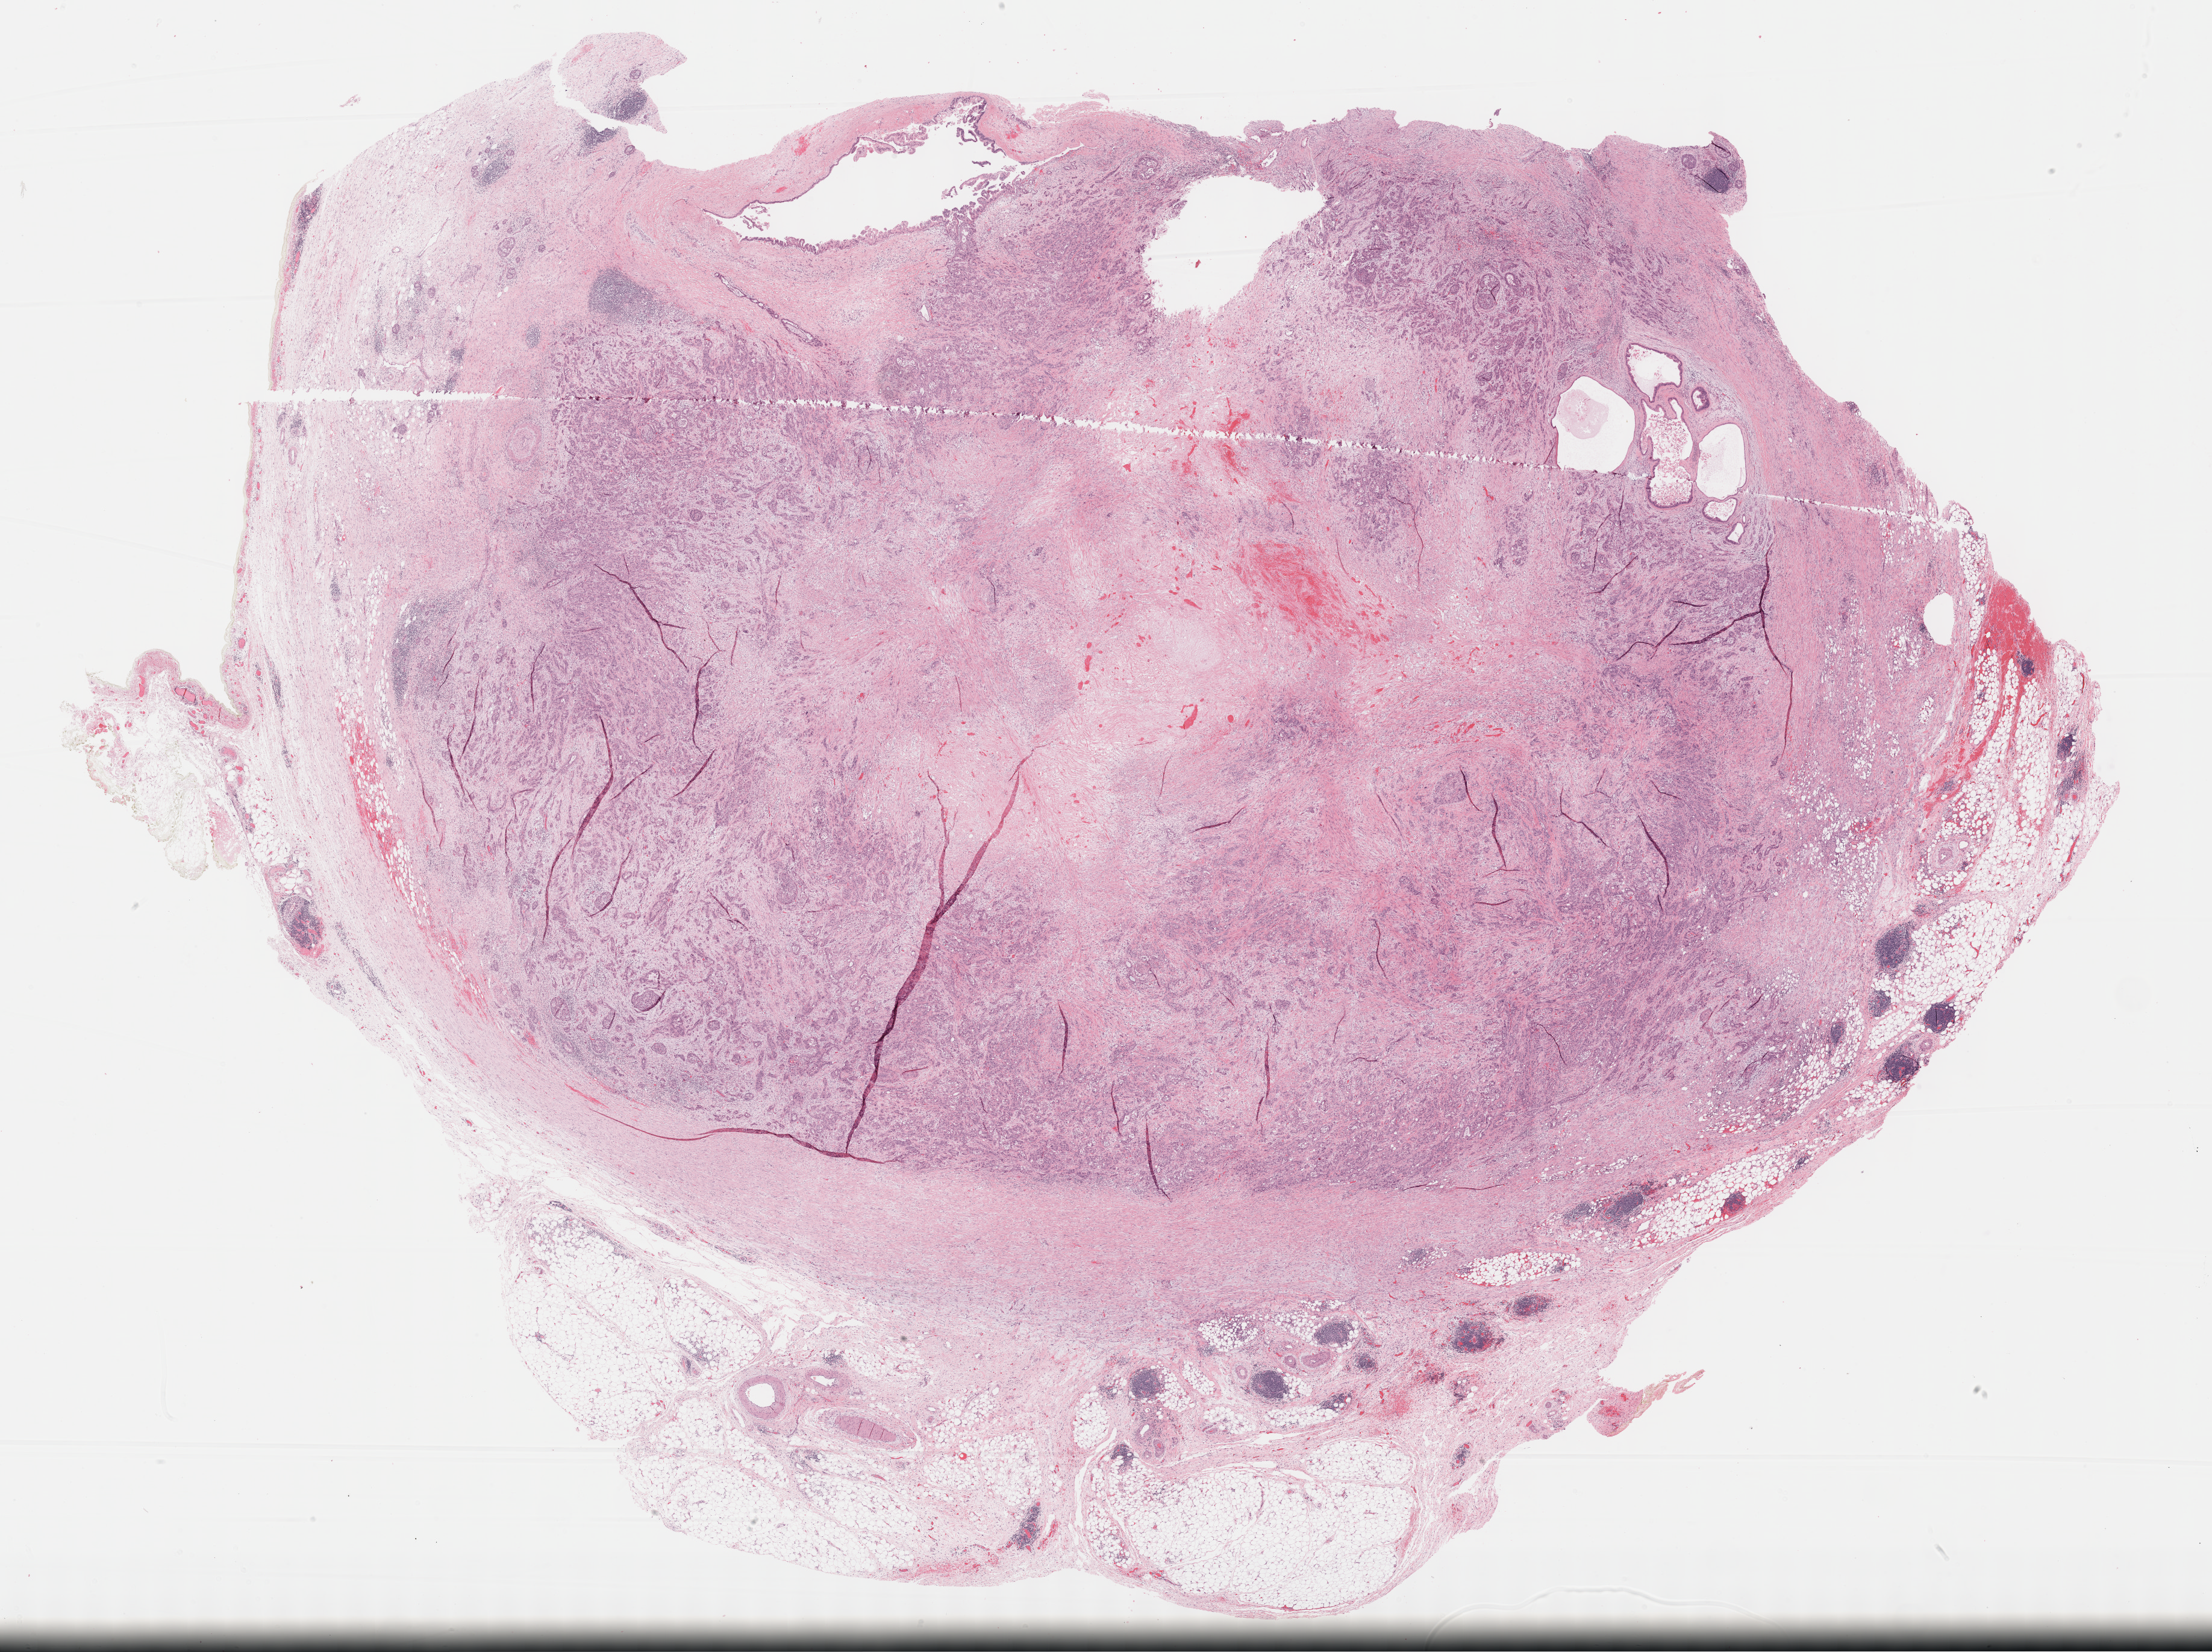
Whole-slide histology image, Hematoxylin and eosin (H&E) stained, low-resolution overview of the scanned area, about 29.7 x 22.2 mm; FFPE section; sample: primary tumour, pancreas. Male, age 64 years at initial diagnosis.
Histologic diagnosis: Infiltrating duct carcinoma, NOS.